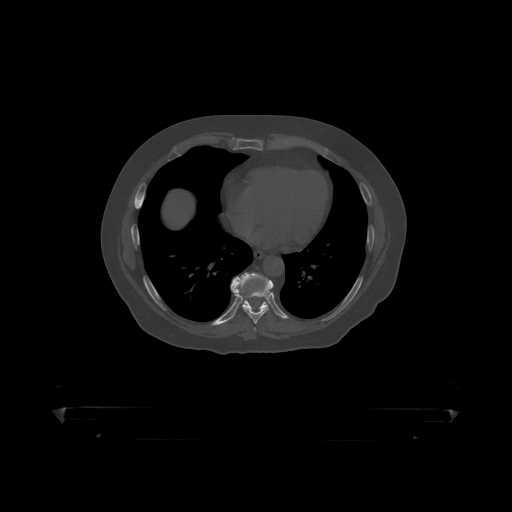
CT including the spine, one axial slice; position 250 of 390 along the scan axis; reconstruction kernel STANDARD; 120 kVp; bone window (W 1800 / L 400 HU); 1.25 mm slice thickness; 512 × 512 image matrix, field of view 650 × 650 mm. Male patient, age 60 years. Case-level facts recorded for this patient, not image findings: primary cancer: prostate.
Outlined on this slice (semi-automatically segmented with operator editing):
- T8 vertebra: box from (x=243, y=280) to (x=274, y=319) px
- T9 vertebra: (x=231, y=273)–(x=268, y=309)